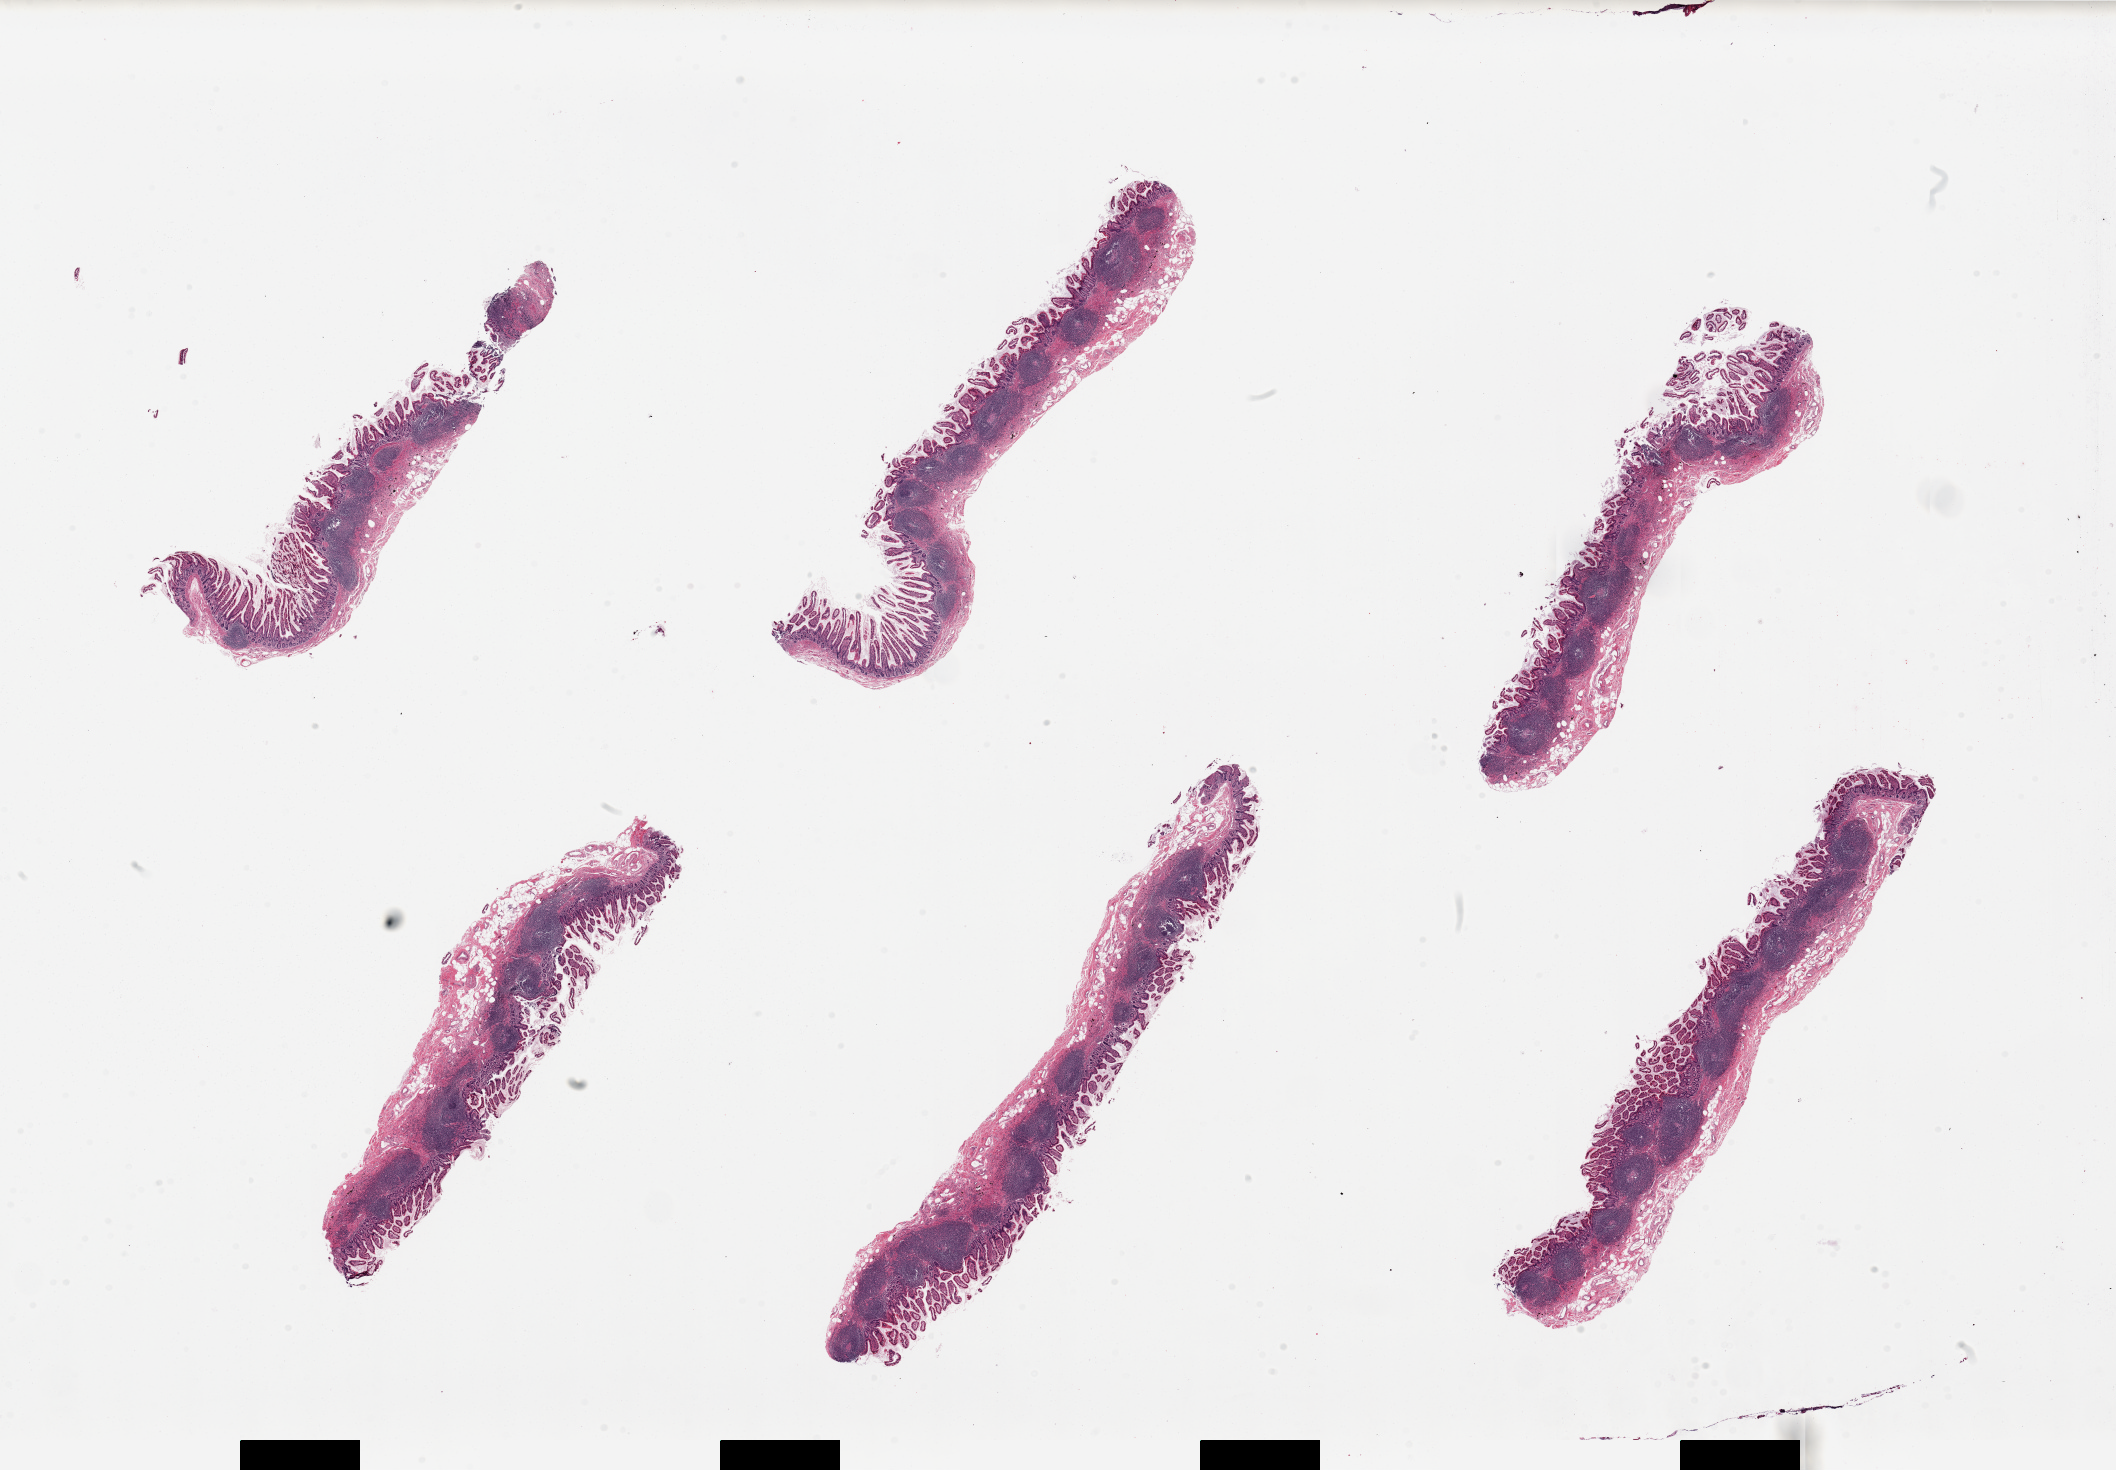
Digitized haematoxylin and eosin-stained section, brightfield — a low-resolution overview of the entire scanned area, about 33.5 x 23.3 mm (from a 20x scan). PAXgene-fixed, paraffin-embedded tissue. Section of ileum (target tissue). Donor tissue sample. Male donor.
Pathologist's review note for this sample: 6 pieces, from 8x2 to 11x1.5mm; excellent lymphoid nodules; mucosa preserved; pigmented macrophages.